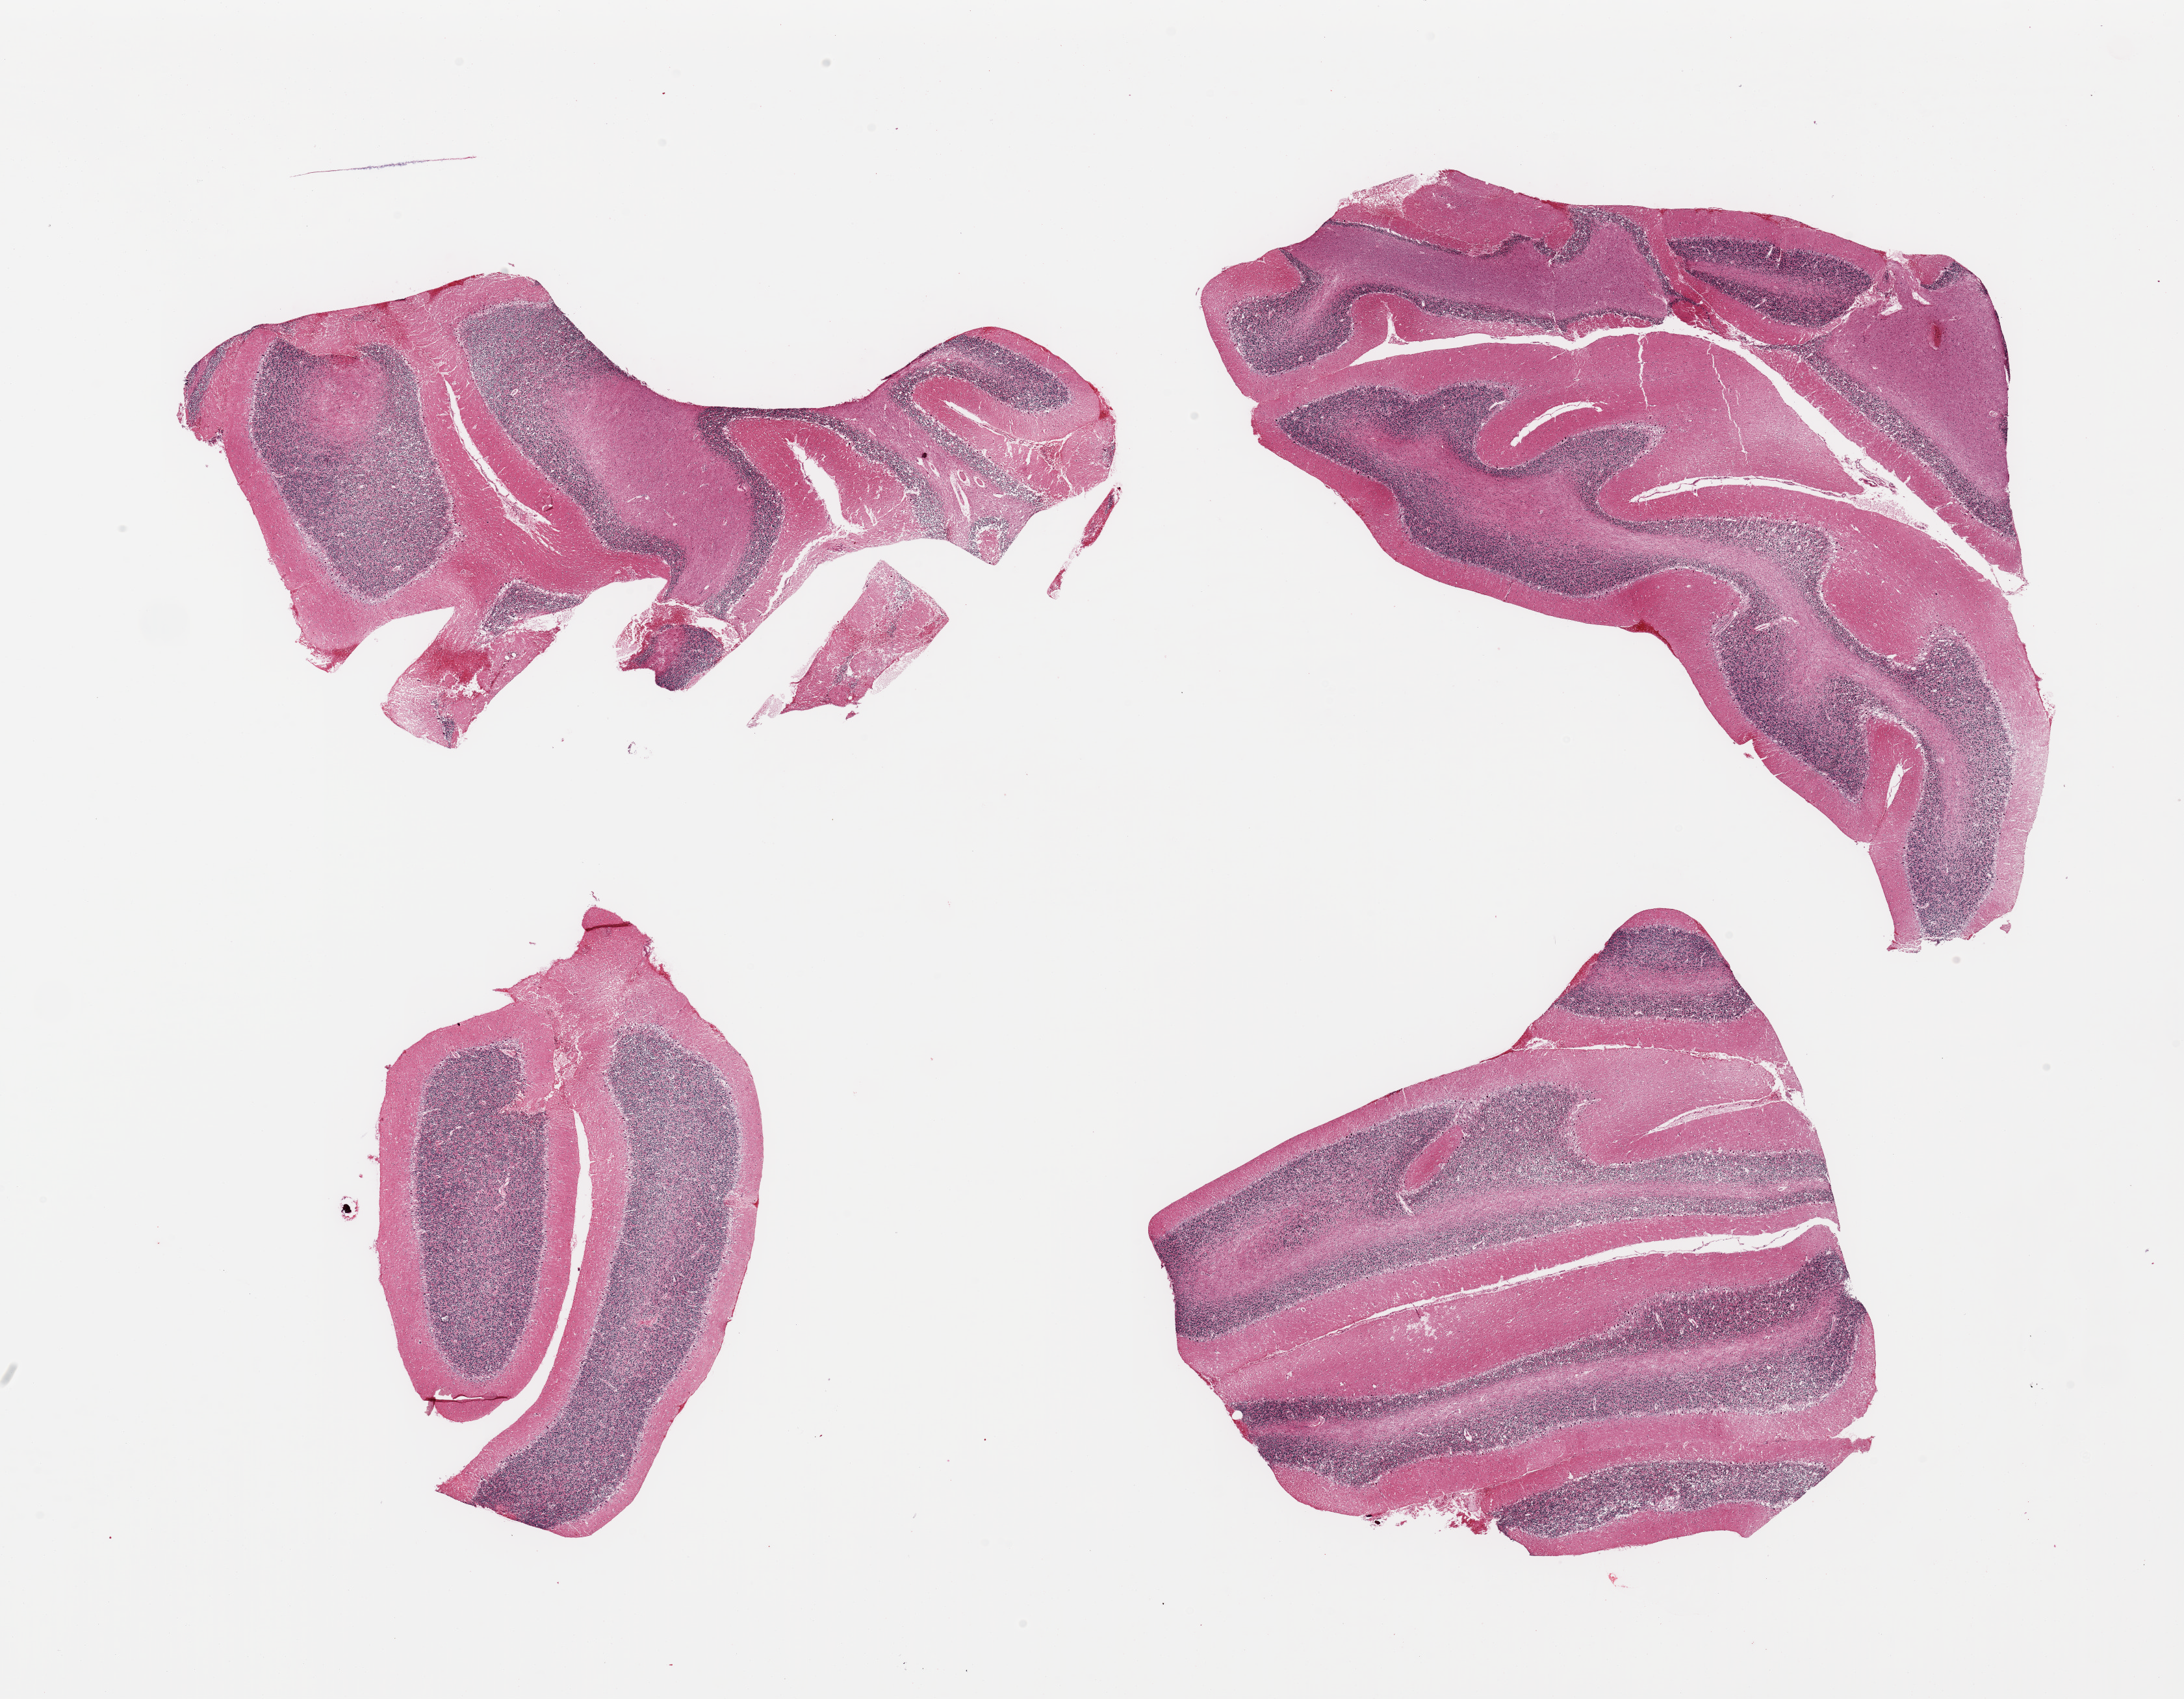
Digitized haematoxylin and eosin-stained section — whole scanned area (about 26.6 x 20.7 mm) shown as a low-resolution overview, PAXgene-fixed, paraffin-embedded tissue, section of cerebellum (target tissue), tissue donor sample. Donor: male.
Pathologist's review note for this sample: 4 pieces.